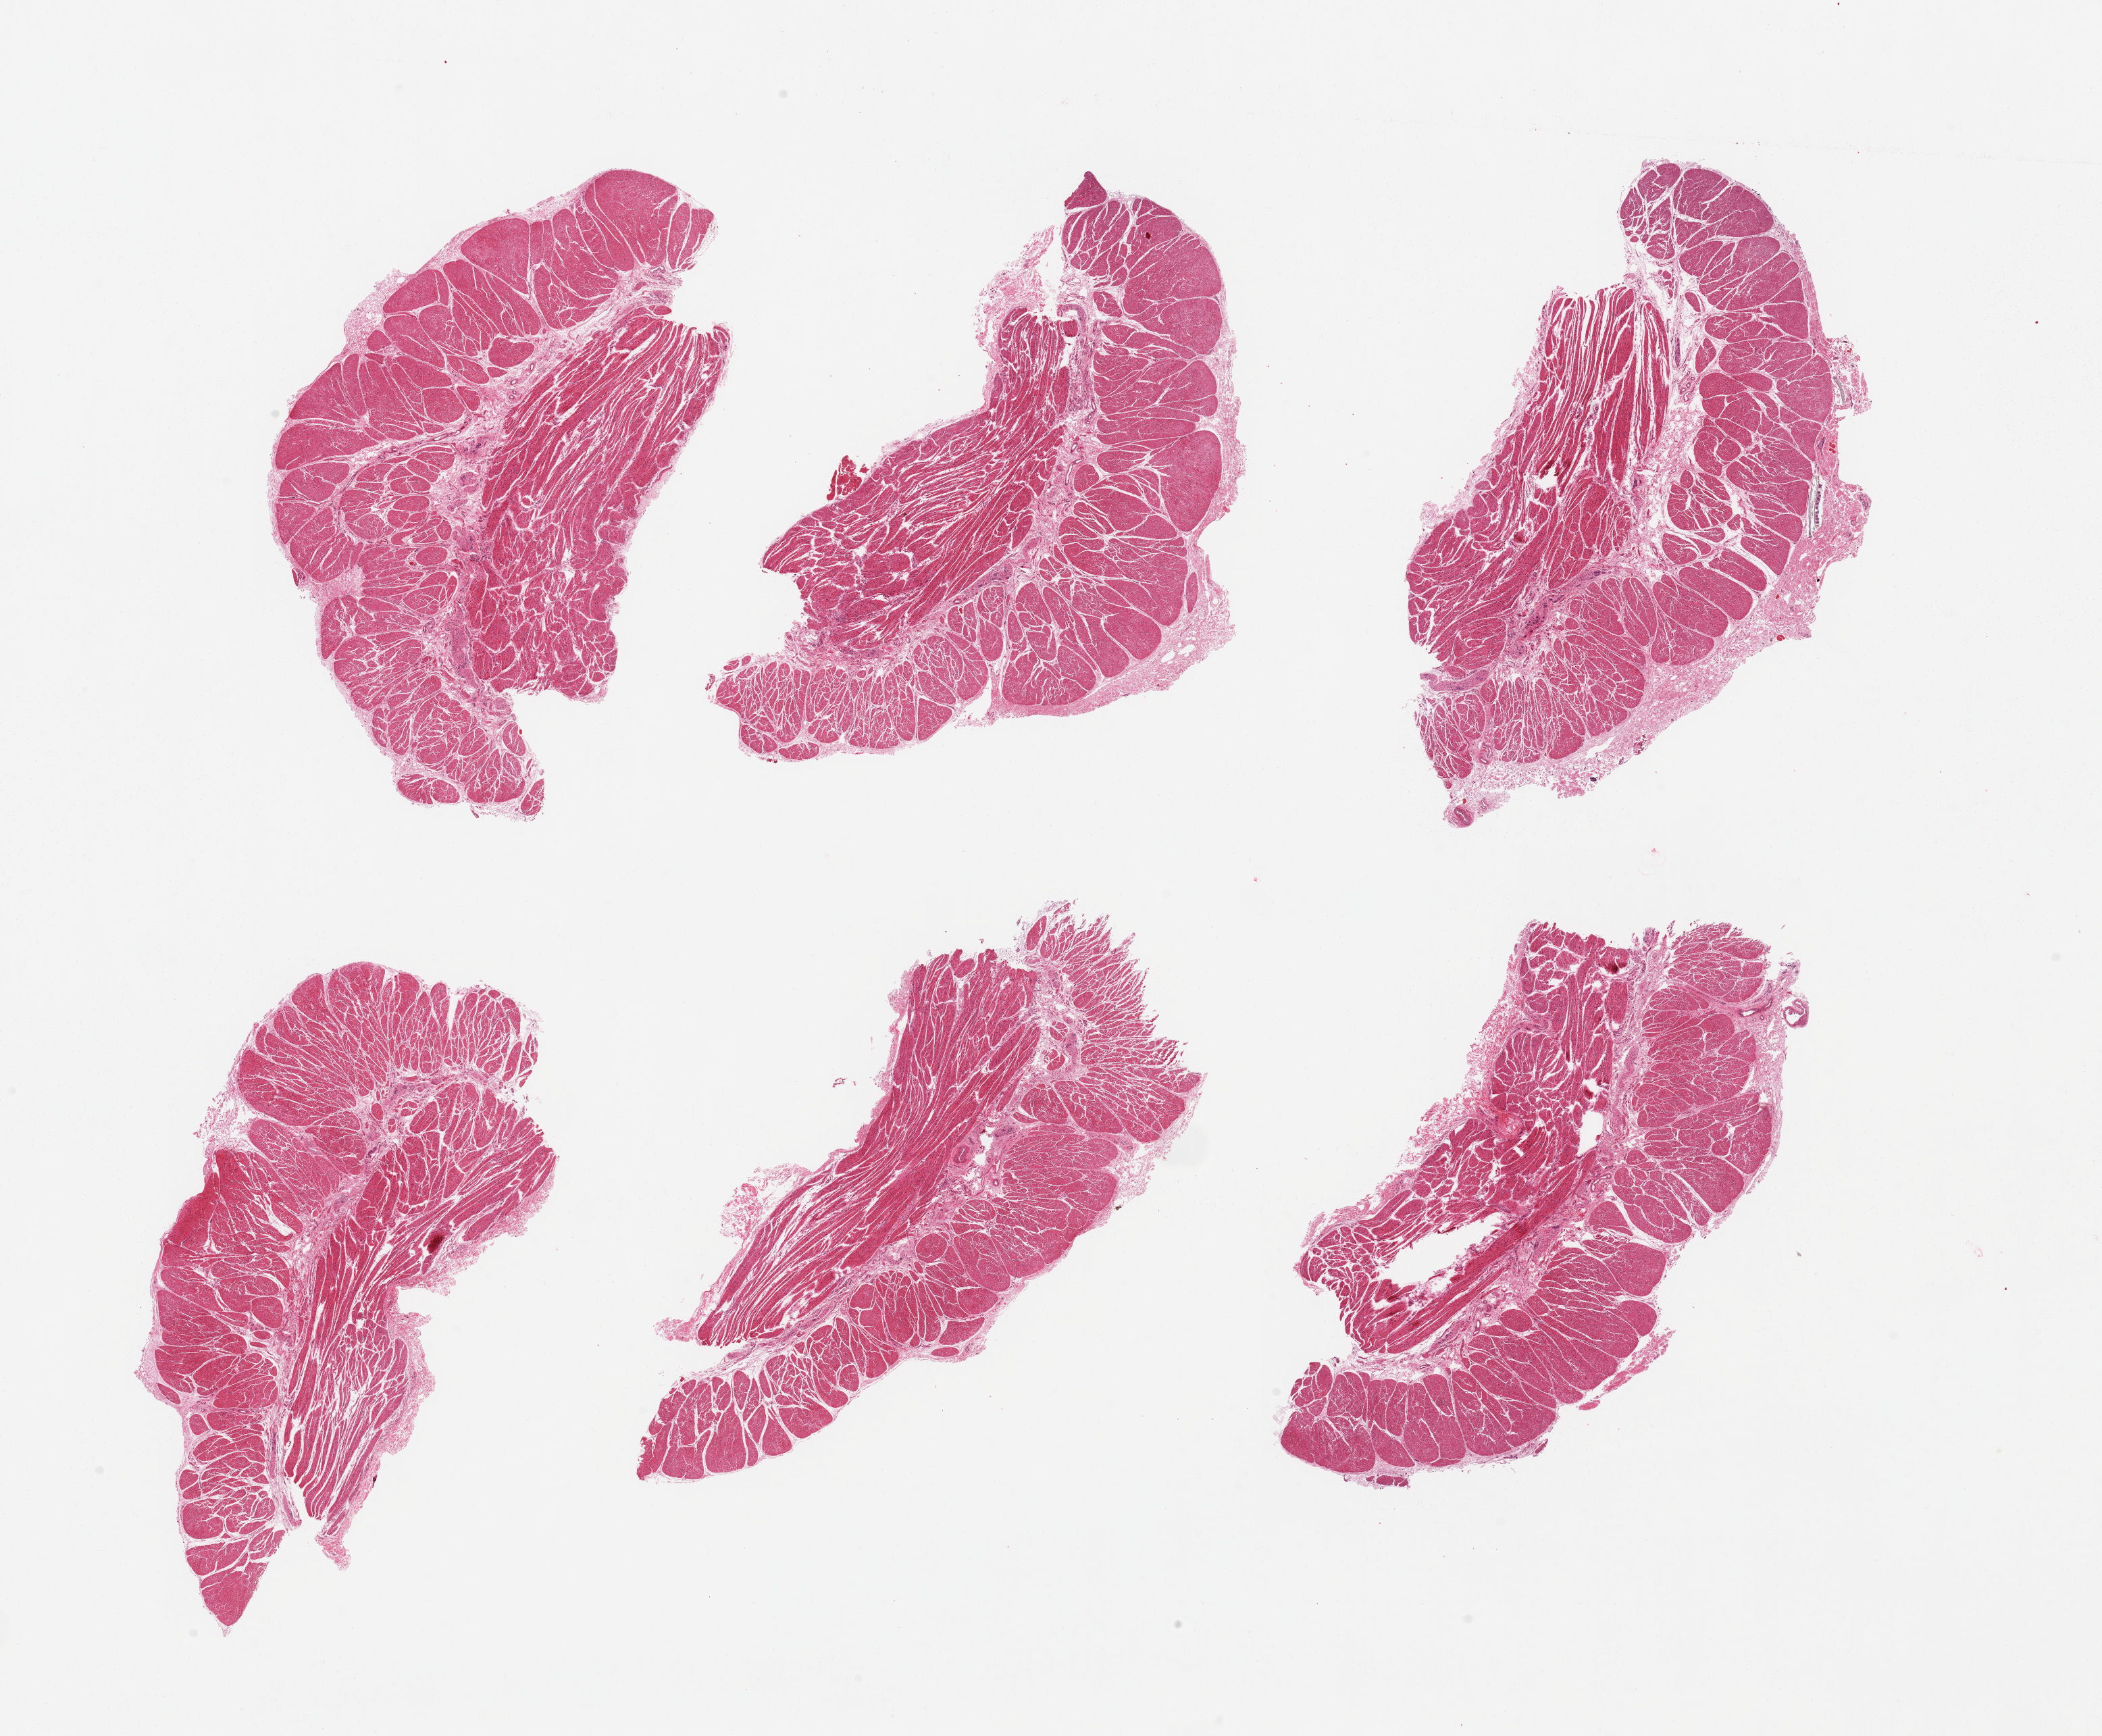
Digitized hematoxylin and eosin (H&E)-stained section, brightfield — shown as a low-resolution overview of the whole scanned area (about 24.6 x 20.3 mm); PAXgene-fixed, paraffin-embedded tissue; target tissue: esophageal muscle; donor tissue sample.
- reviewer comment on this tissue sample: 6 pieces; well dissected muscularis